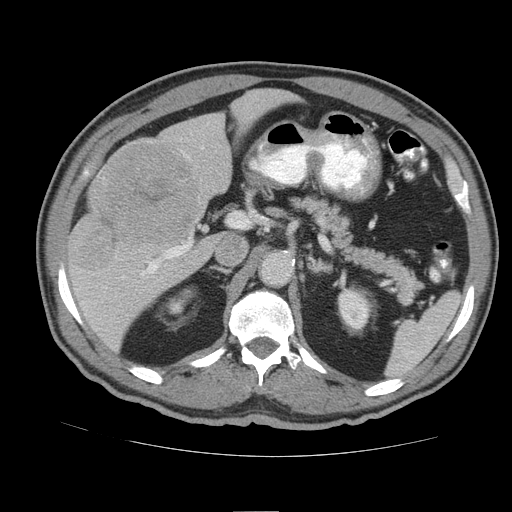
Contrast-enhanced abdominal CT (liver protocol), one axial slice. Position 51 of 105 along the scan axis. 140 kVp. Soft-tissue window (W 400 / L 40 HU). 512 × 512 image matrix, field of view 380 × 380 mm. Case-level facts recorded for this patient, not image findings: diagnosis: hepatocellular carcinoma (patient treated with transarterial chemoembolisation; whether this scan precedes or follows treatment is not stated here); TNM stage (as recorded): Stage-IIIB; Child-Pugh class: A; tumour nodularity: multinodular.
Annotated regions visible in this slice (semi-automatically segmented with operator editing):
- liver parenchyma outside the tumour (the mass and vessels are separate outlines, so this box may not span the whole liver): bounding box [x1, y1, x2, y2] px = [68, 88, 290, 352]
- mass: [73, 142, 200, 269]
- liver vessels: [83, 147, 204, 303]